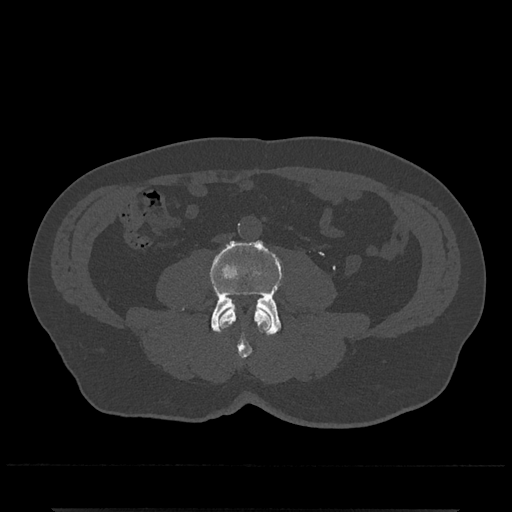
CT including the spine, one axial slice. Position 180 of 797 along the scan axis. Reconstruction kernel Br40s/3. 120 kVp. Bone window (W 1800 / L 400 HU). 512 × 512 image matrix. Male patient, age 67 years. From the clinical record (not read from this slice): primary cancer: prostate.
Outlined on this slice (semi-automatic segmentation, software-assisted and operator-edited):
- L3 vertebra: bounding box <219,307,272,359> (left, top, right, bottom; pixels)
- L4 vertebra: <210,240,284,336>